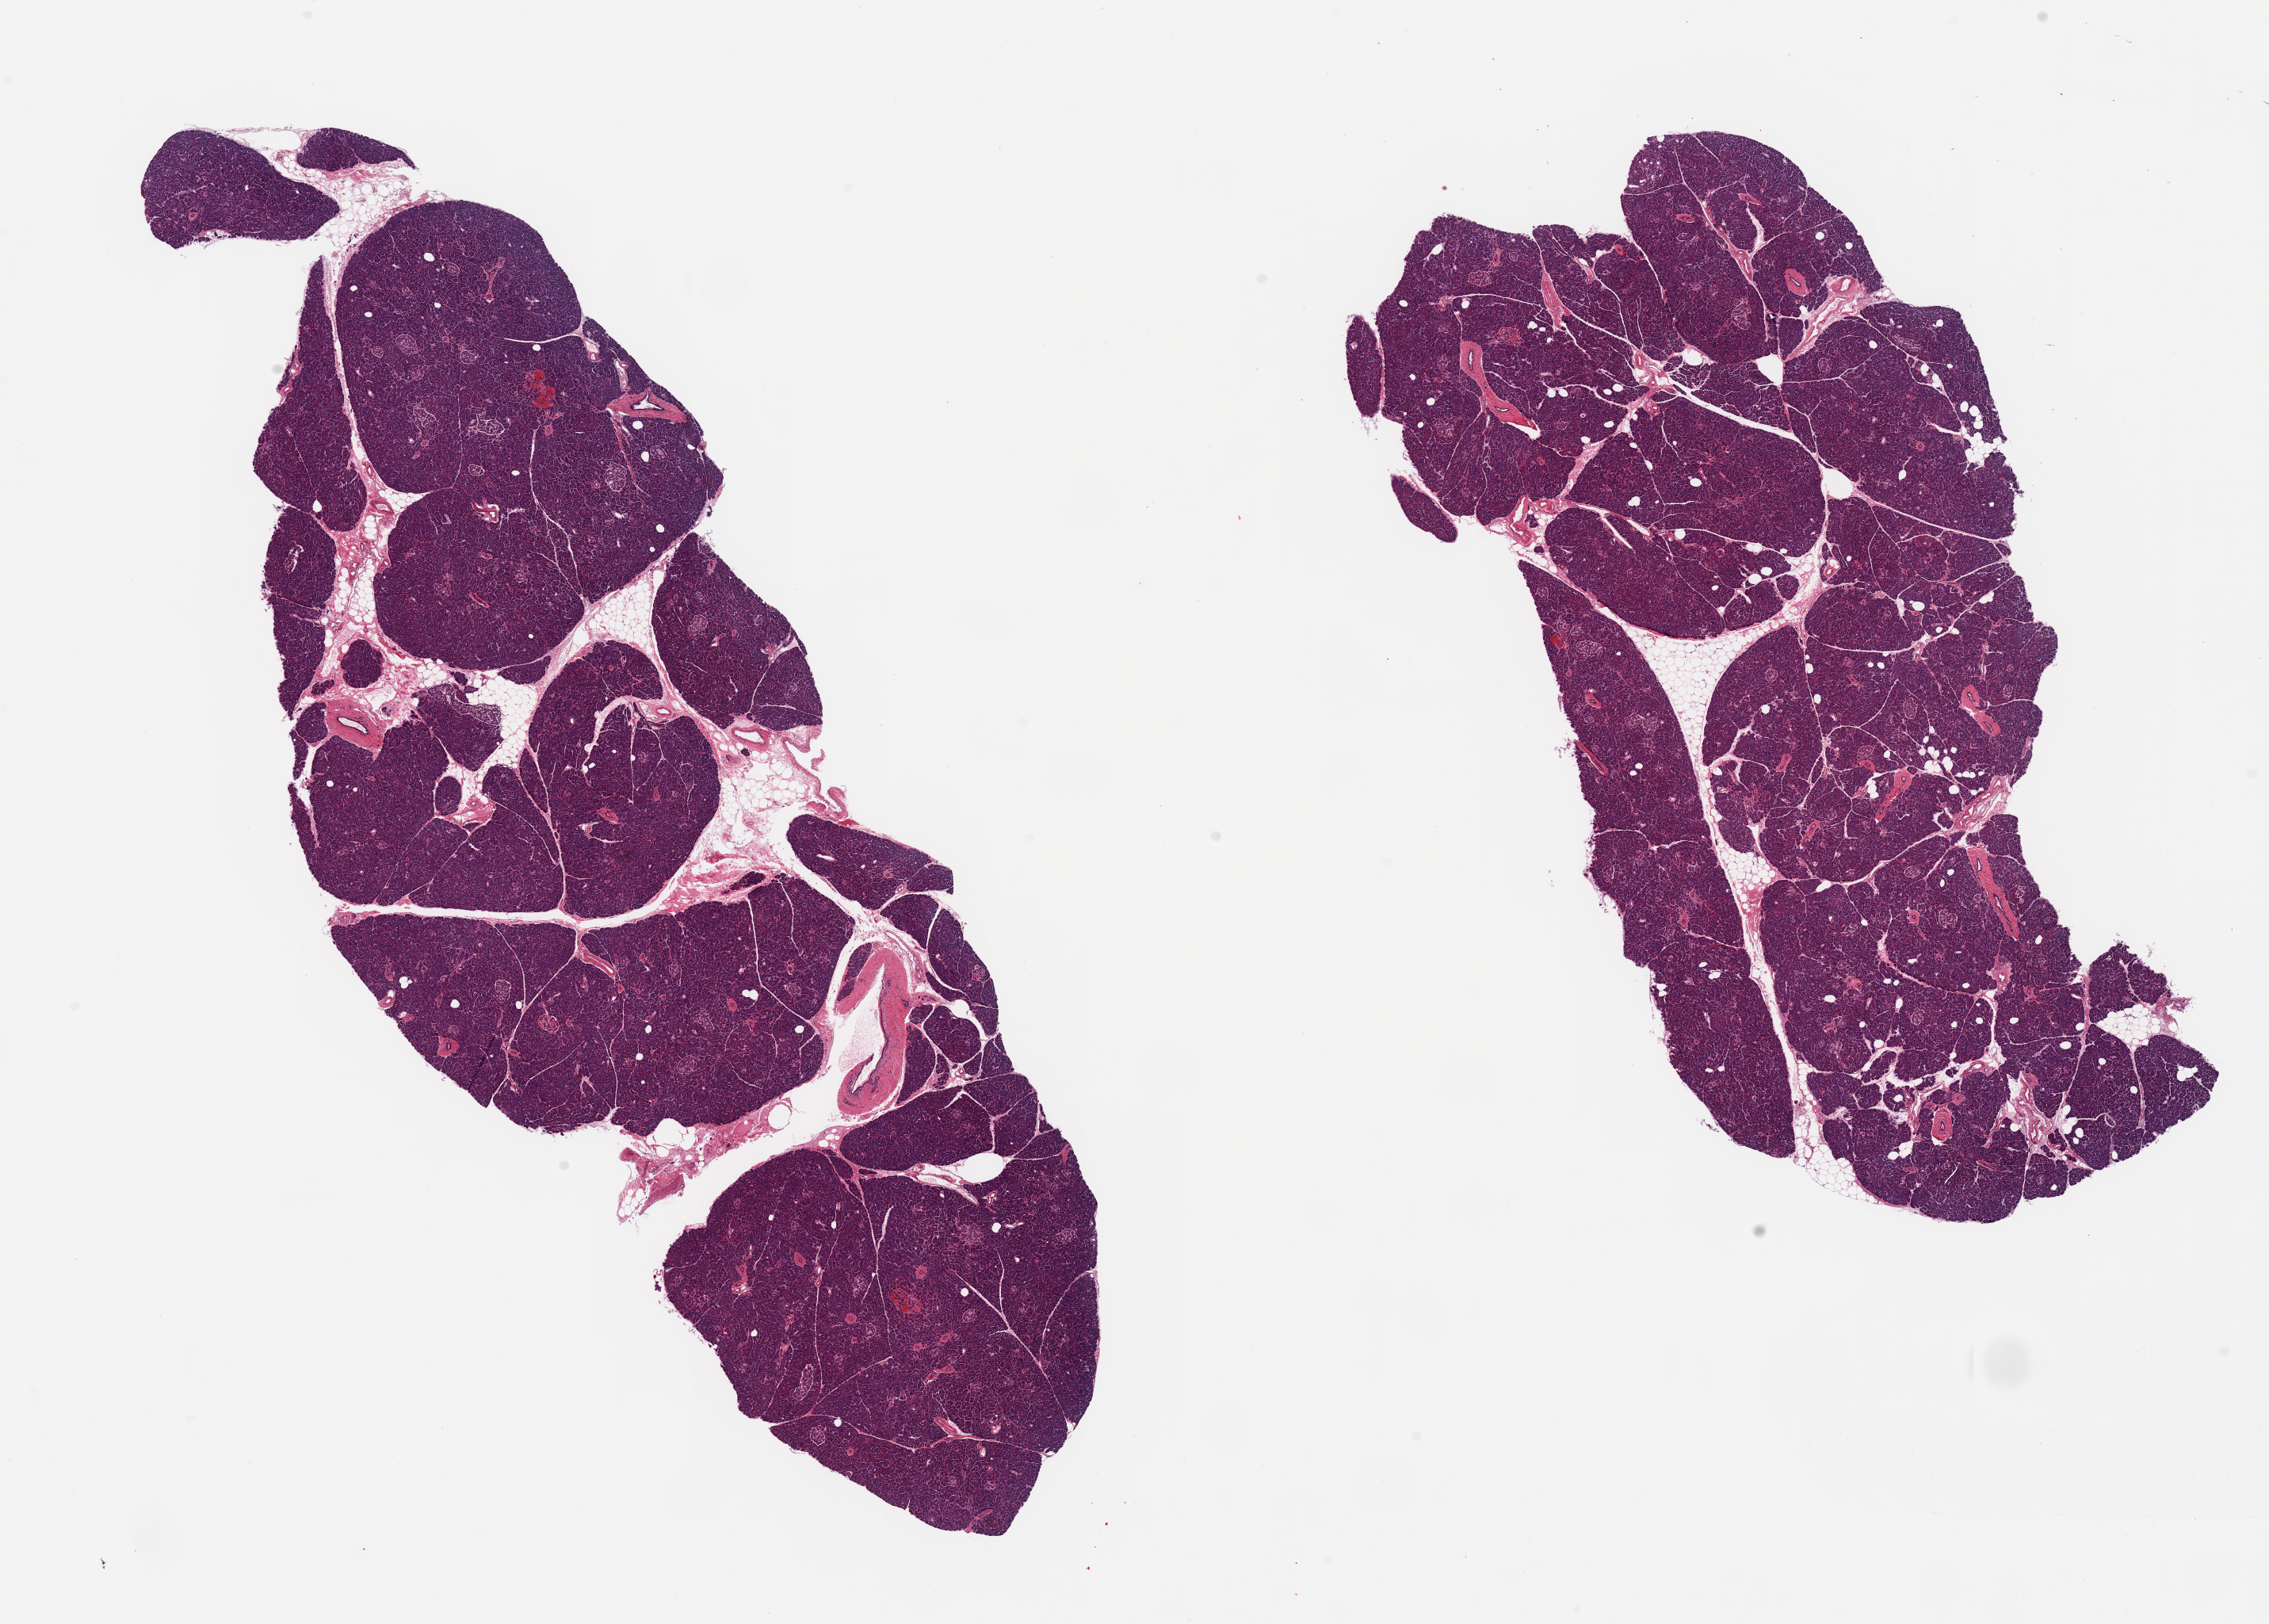
Haematoxylin and eosin whole-slide image, brightfield, a low-resolution overview of the entire scanned area, about 22.6 x 16.2 mm. PAXgene-fixed, paraffin-embedded tissue. Target tissue: pancreas. Donor tissue sample. Donor sex: male.
Review note (as recorded): 2 pieces, well preserved Islets present.